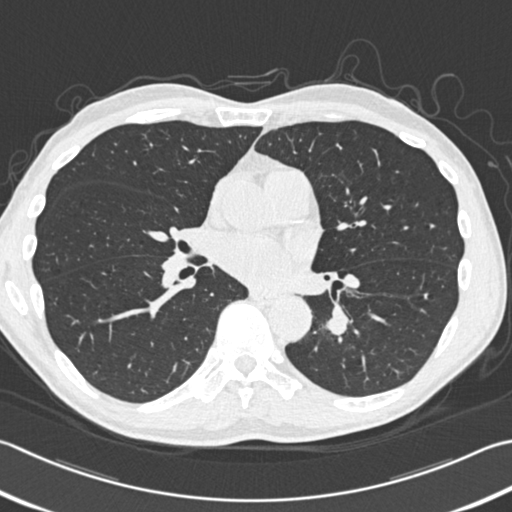
Low-dose screening chest CT, one axial slice; position 174 of 354 along the scan axis; reconstruction kernel B30f; 120 kVp; lung window (W 1500 / L -600 HU); 1 mm slice thickness; 512 × 512 image matrix, field of view 346 × 346 mm.
Outlined on this slice (manually delineated by an expert):
- lesion 1 (tumor, lower lobe of left lung): bounding box (x1, y1, x2, y2) in pixels: (327, 316, 348, 335)